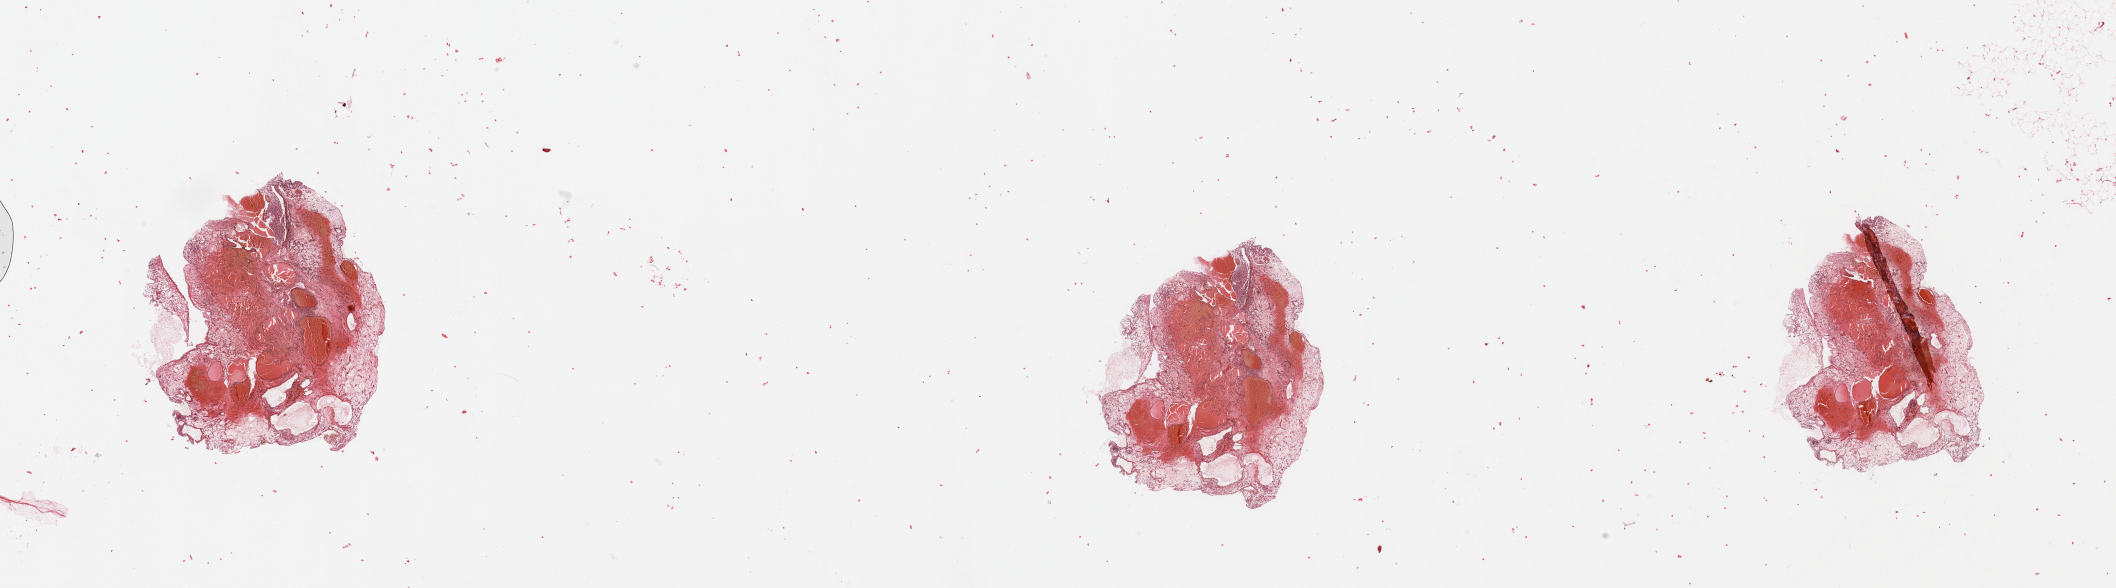
Digitized H&E tissue section (whole slide), low-resolution overview of the scanned area, about 33.5 x 9.3 mm (slide scanned at 20x); tumour tissue sample, kidney. Patient: male, age 74 years. Histologic grade: G1 (well differentiated).
• primary tumour site (as recorded): middle
• diagnosis: Renal cell carcinoma, NOS
• AJCC pathologic stage: I